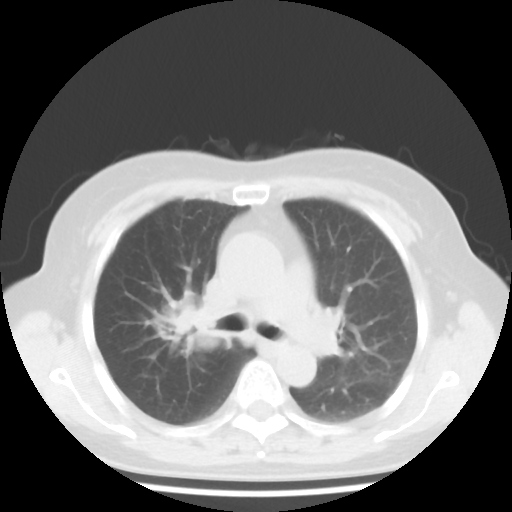
Chest CT, one axial slice; slice 26 of 43 in the series (ordered by position); reconstruction kernel STANDARD; 100 kVp; lung window (W 1500 / L -600 HU); 5 mm slice thickness; 512 × 512 image matrix. Female patient, age 62 years. Case-level facts recorded for this patient, not image findings: clinical TNM (as recorded): T3 N0 M0.
Outlined on this slice (bounding box drawn by a radiologist):
- lung tumour (recorded histology: small cell carcinoma): bounding box <161,293,228,357> (left, top, right, bottom; pixels)